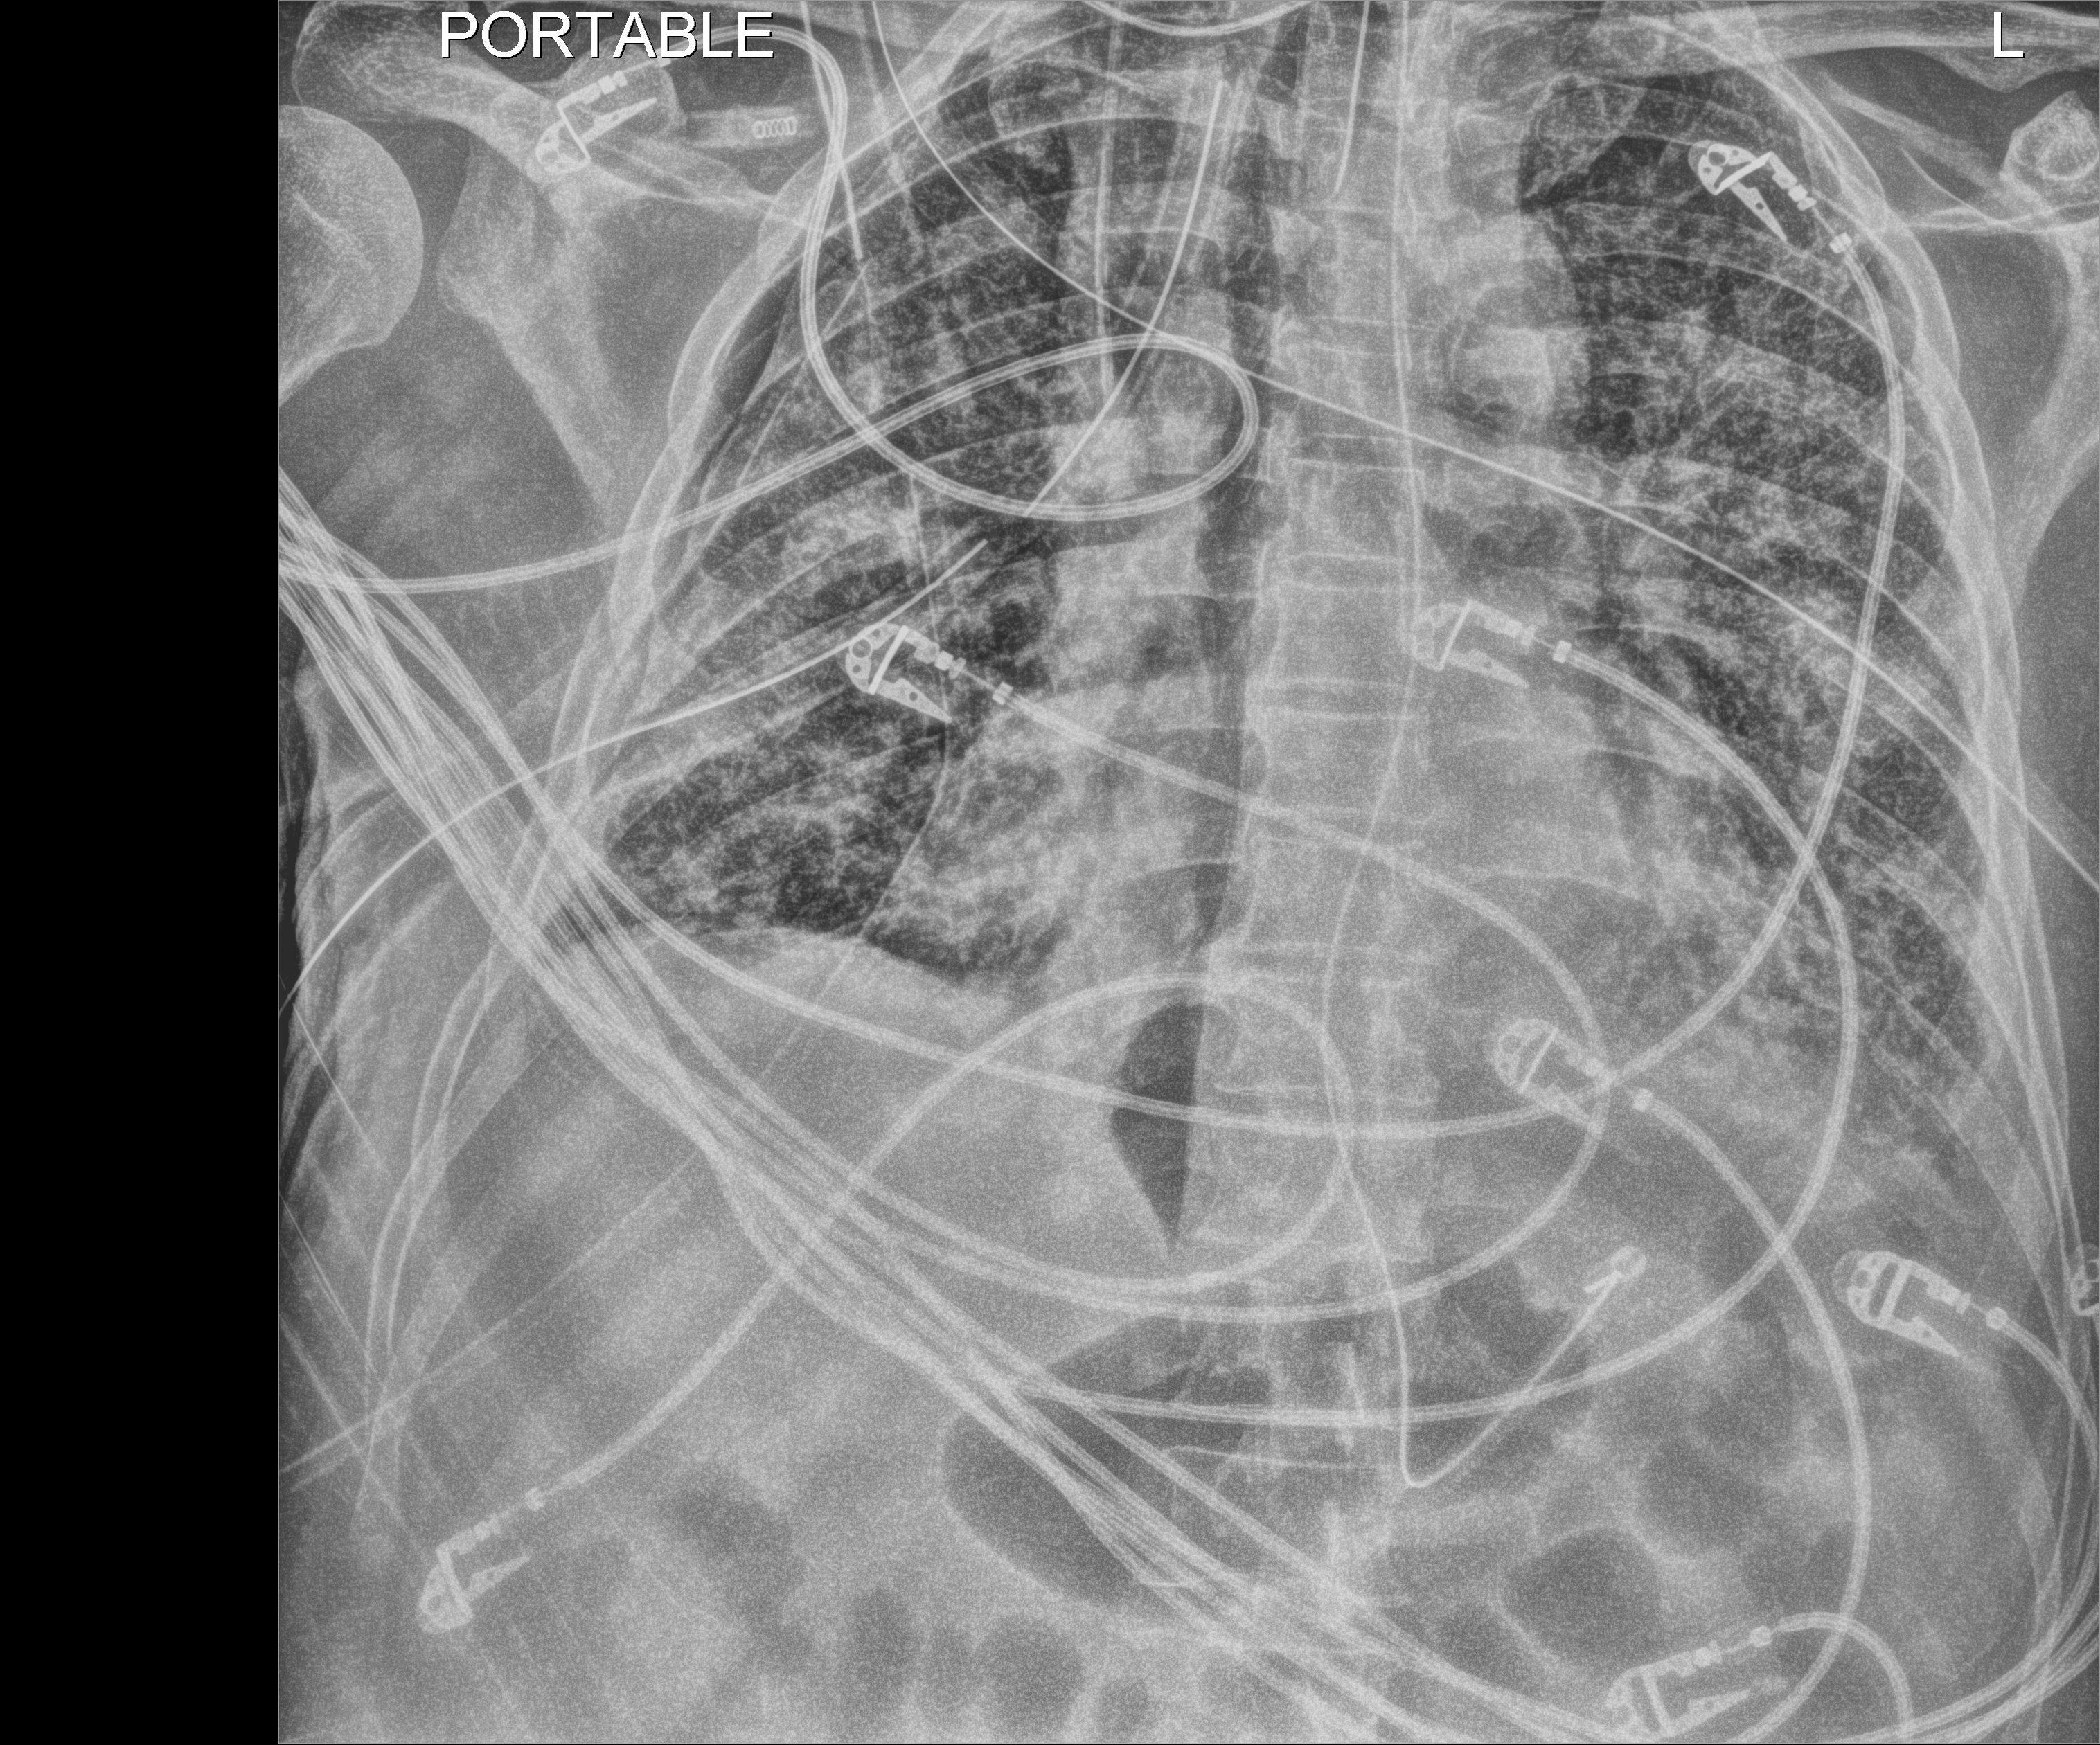
Chest X-ray (portable); anteroposterior (AP) projection. Male patient hospitalised with COVID-19, age 60–74 years.
Admission-level facts for this patient (not findings on this image; timing relative to this image not recorded): admitted to intensive care during this hospital stay: yes.